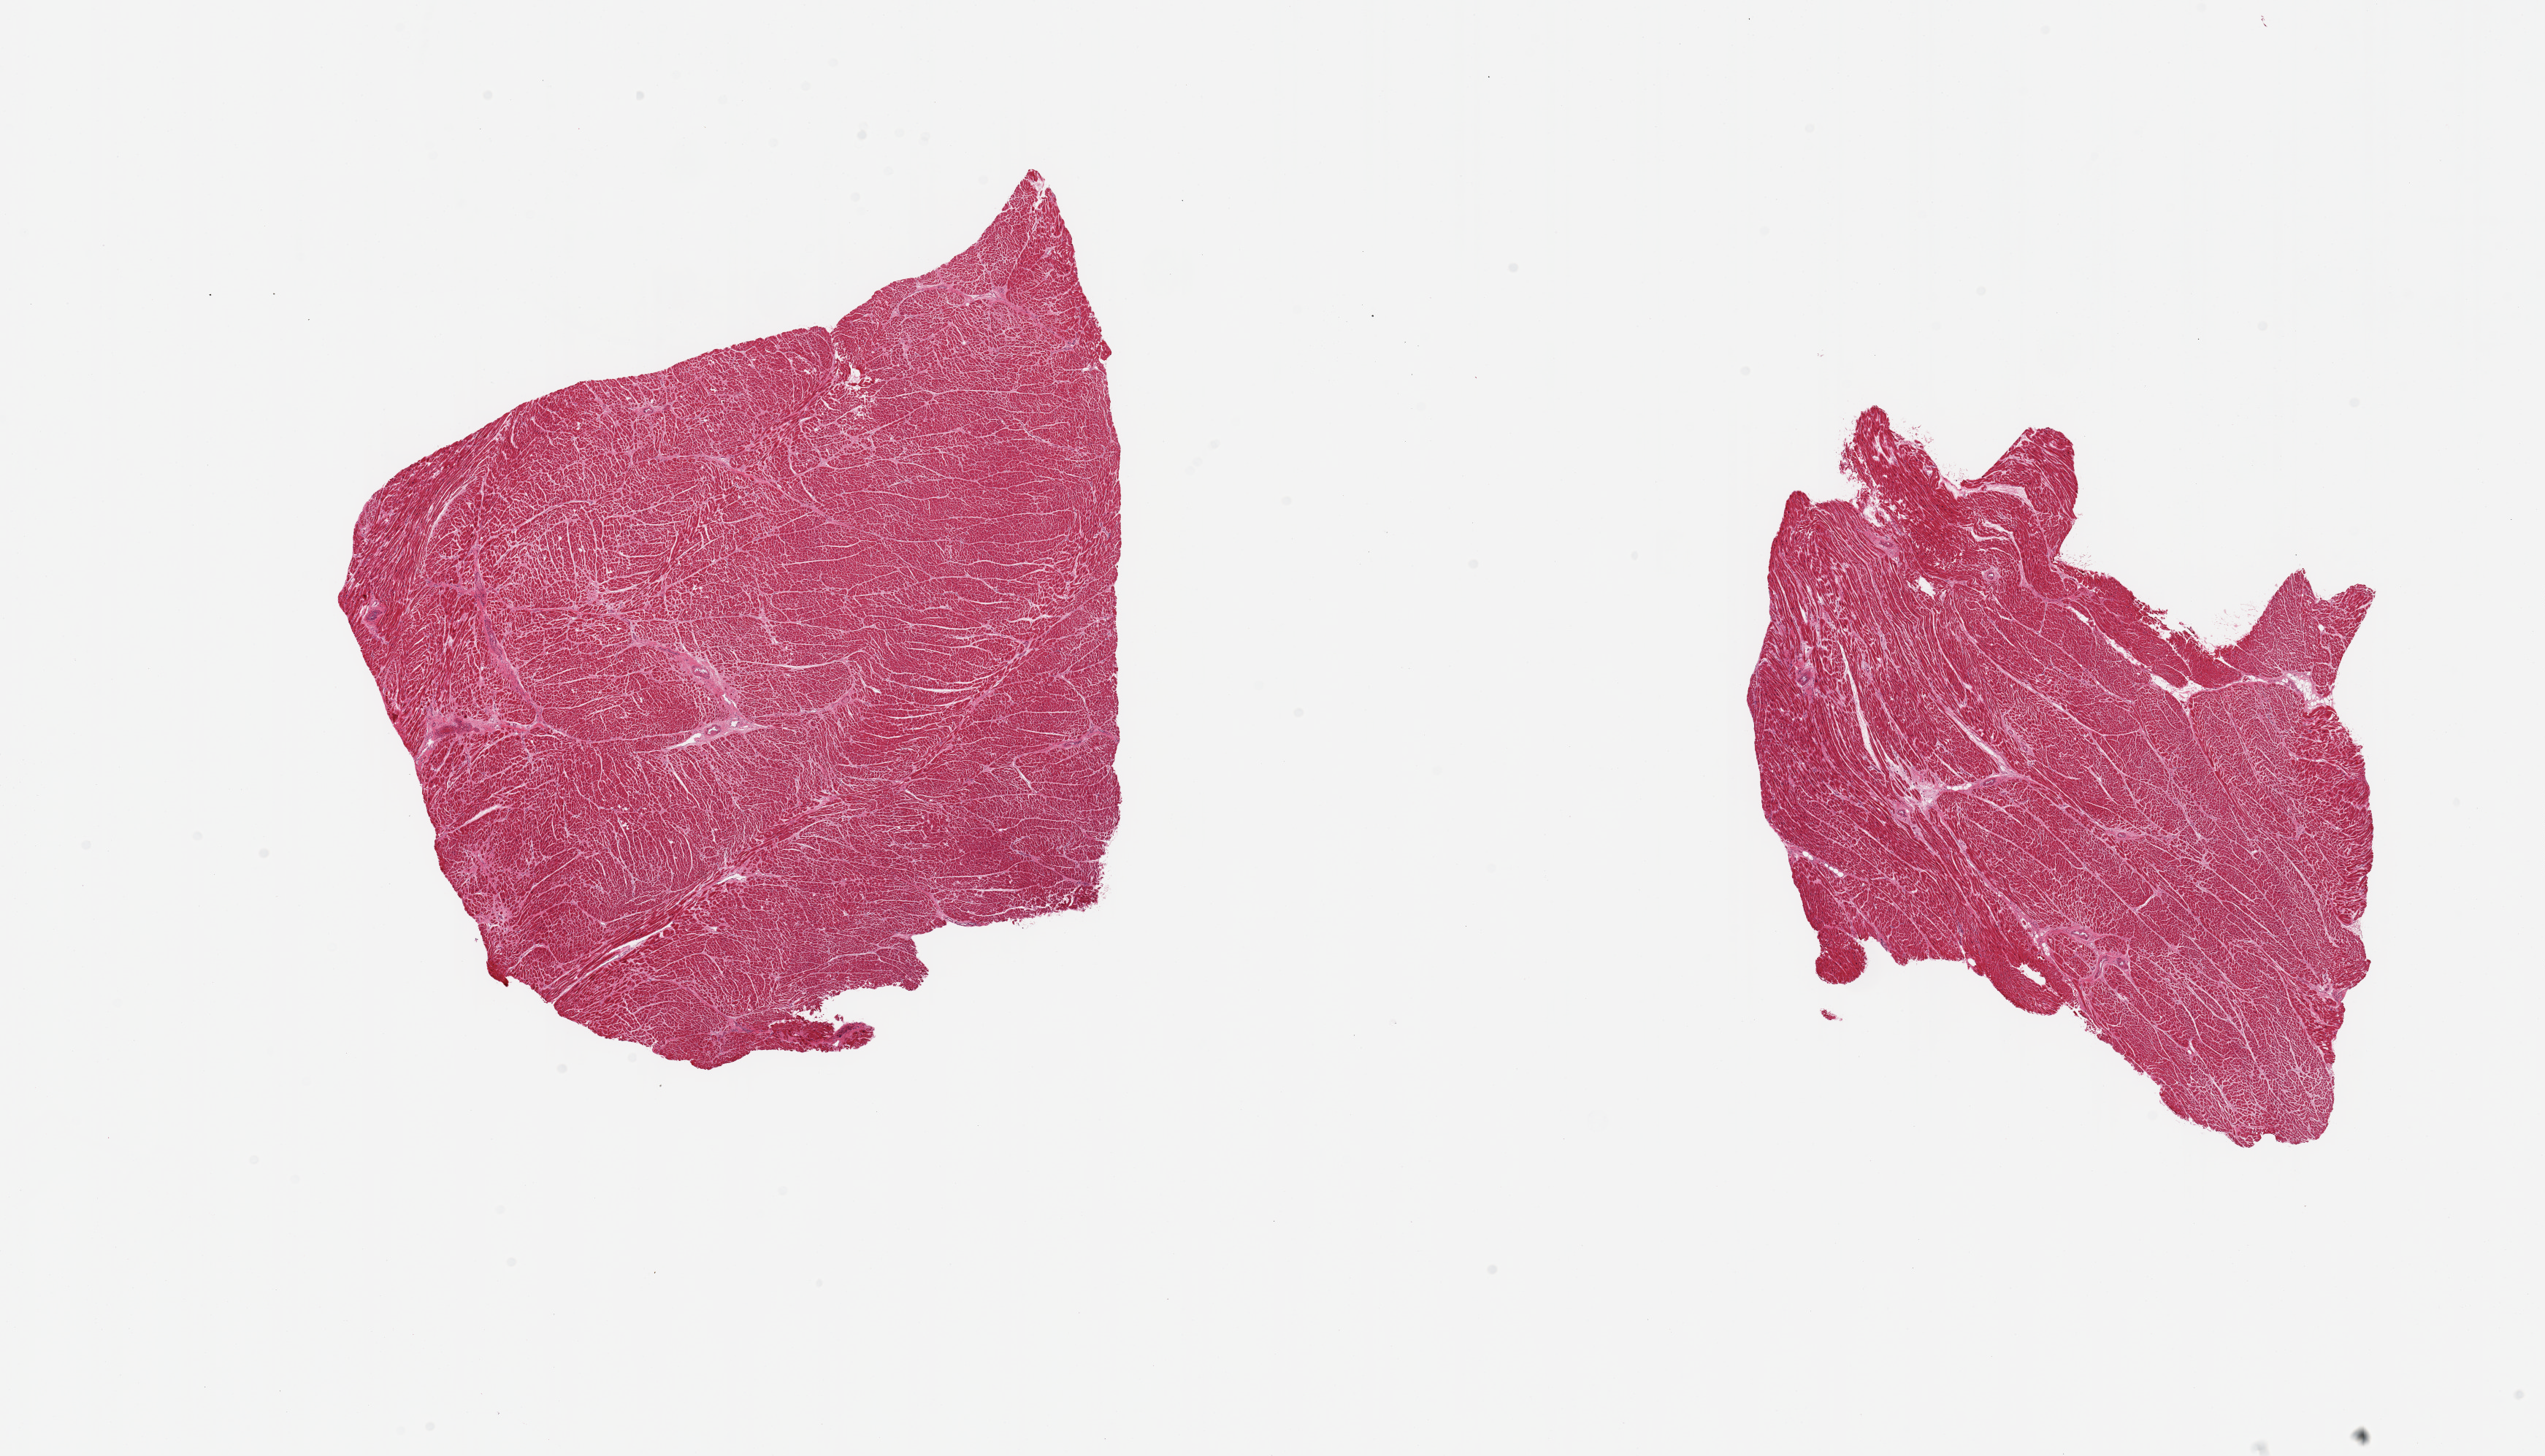
H&E whole-slide image — shown as a low-resolution overview of the whole scanned area (about 27.6 x 15.8 mm, acquisition: 20x scan). PAXgene-fixed, paraffin-embedded tissue. Target tissue: heart. Donor tissue sample. Male donor.
Reviewer comment on this tissue sample: 2 pieces, mild - moderate interstitial fibrosis, few microinfarcts.